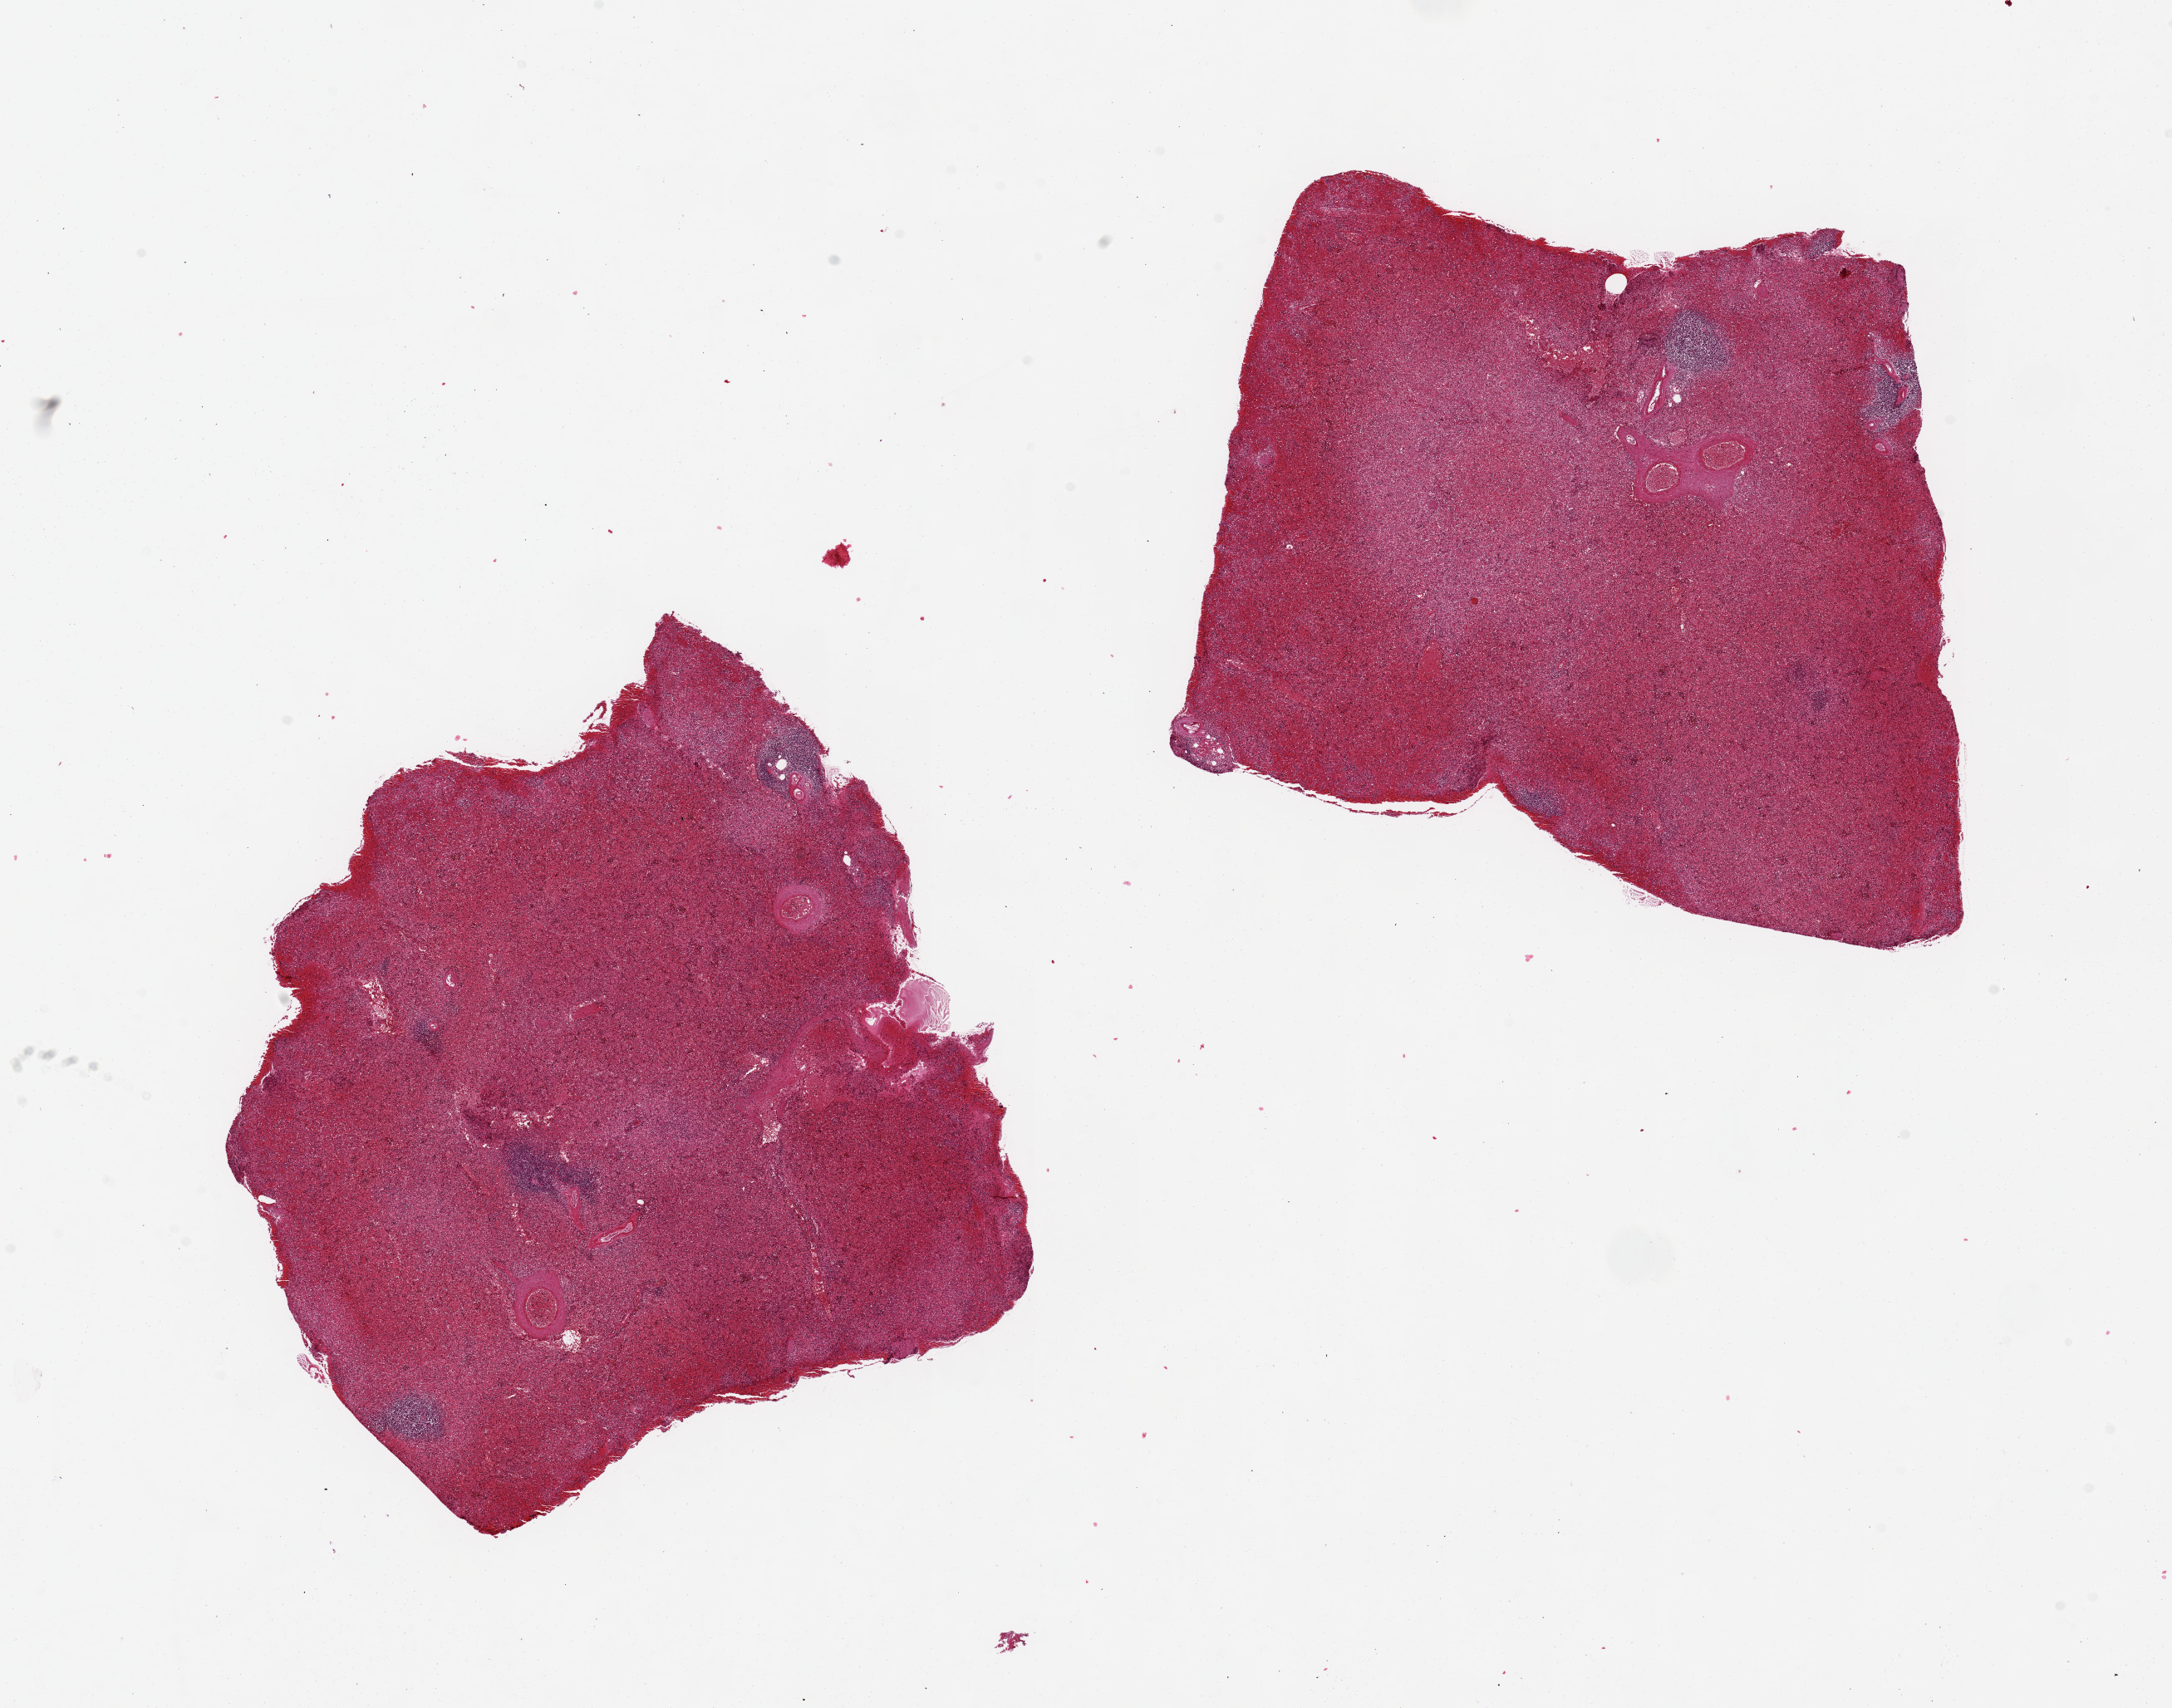
Haematoxylin and eosin whole-slide image, brightfield, whole scanned area (about 20.7 x 16.3 mm, acquisition: 20x scan) shown as a low-resolution overview, PAXgene-fixed, paraffin-embedded tissue, section of spleen (target tissue), donor tissue sample.
* pathologist's review note for this sample: 2 pieces, both 6.8x6.5 mm; congested and autolyzed